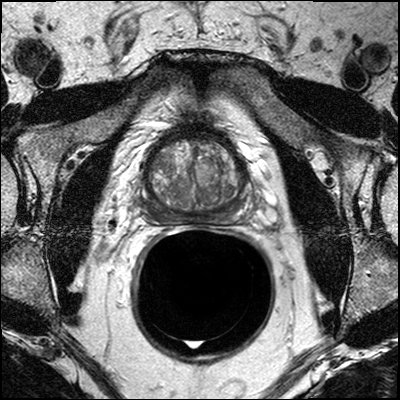
MRI of the prostate; 3 images, each a single mid-volume slice chosen by position (not for content). Treatment context recorded for this patient: Surgery.
Image 1: axial T2-weighted image, series "T2W_TSE_AX", slice 17 of 32.
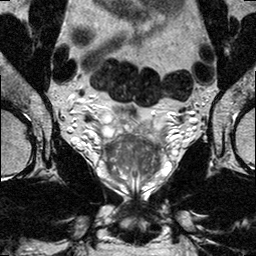
Image 2: T2-weighted coronal slice, slice 17 of 32.
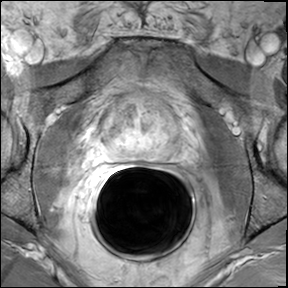
Image 3: DCE (dynamic gadolinium-enhanced) axial slice, series "AX BLISS_GAD_8", slice 17 of 32, dynamic phase 5 of 8.
Radiologist's MRI report for this examination:
prostate has a maximal lateral diameter of 5.6 cm, a maximal craniocaudal diameter of 4.5 cm and a maximal AP diameter of 4.1 cm resulting in an estimated gland volume of 54 cc. The zonal anatomy is preserved. There is a 11 x 9 x 9 mm T2-hypo intense dominant mass seen in the right posterior lateral peripheral zone of prostate base and midthird. The mass shows suspicious enhancement, which is confined to the prostatic borders. The adjacent right neurovascular bundle is not involved. No evidence for involvement of the neurovascular bundle on either side. No evidence for seminal vesicles infiltration. No evidence of involvement of bladder neck and rectal wall. No suspiciously enlarged obturator and iliac lymph nodes. There is a prominent venous plexus. There is BPH. IMPRESSION: Right sided prostate cancer in the mid third and base of the prostate, with dominant nodule (11 x 9 x 9 mm) in the right posterior lateral peripheral zone. No evidence of extracapsular extension. There is a prominent venous plexus.

Biopsy pathology report for this patient (as recorded):
Biopsy: Specimen consists of multiple brown/tan core biopsies measuring in length from 0.5 cm to 2.3 cm and 0.1 cm in diameter each. The specimen is submitted in toto in seven cassettes as follows: 1 right PZ, 2 right PZ/TZ, 3 right apex, 4 left PZ, 5 left PZ/TZ, 6 left apex PROSTATE BIOPSIES: 1. RIGHT PZ: PROSTATIC ADENOCARCINOMA, GLEASON SCORE 3+3=6/10, INVOLVING 1 OF 1 CORE, AND 30% OF TOTAL TISSUE. 2. RIGHT PZ/TZ: PROSTATIC ADENOCARCINOMA, GLEASON SCORE 3+4=7/10, INVOLVING 3 OF 3 CORES, AND 20% OF TOTAL TISSUE. 3. RIGHT APEX: PROSTATIC ADENOCARCINOMA, GLEASON SCORE 3+3=6/10, INVOLVING 1 OF 1 CORE, AND <5% OF TOTAL TISSUE. 4. LEFT PZ: BENIGN PROSTATIC TISSUE. 5. LEFT PZ/TZ: BENIGN PROSTATIC TISSUE. 6. LEFT APEX: BENIGN PROSTATIC TISSUE. 7. FLOATER: PROSTATIC ADENOCARCINOMA, GLEASON SCORE 3+3=6/10, INVOLVING 1 of 2 CORES, AND 20% OF TOTAL TISSUE. and 7 floater.